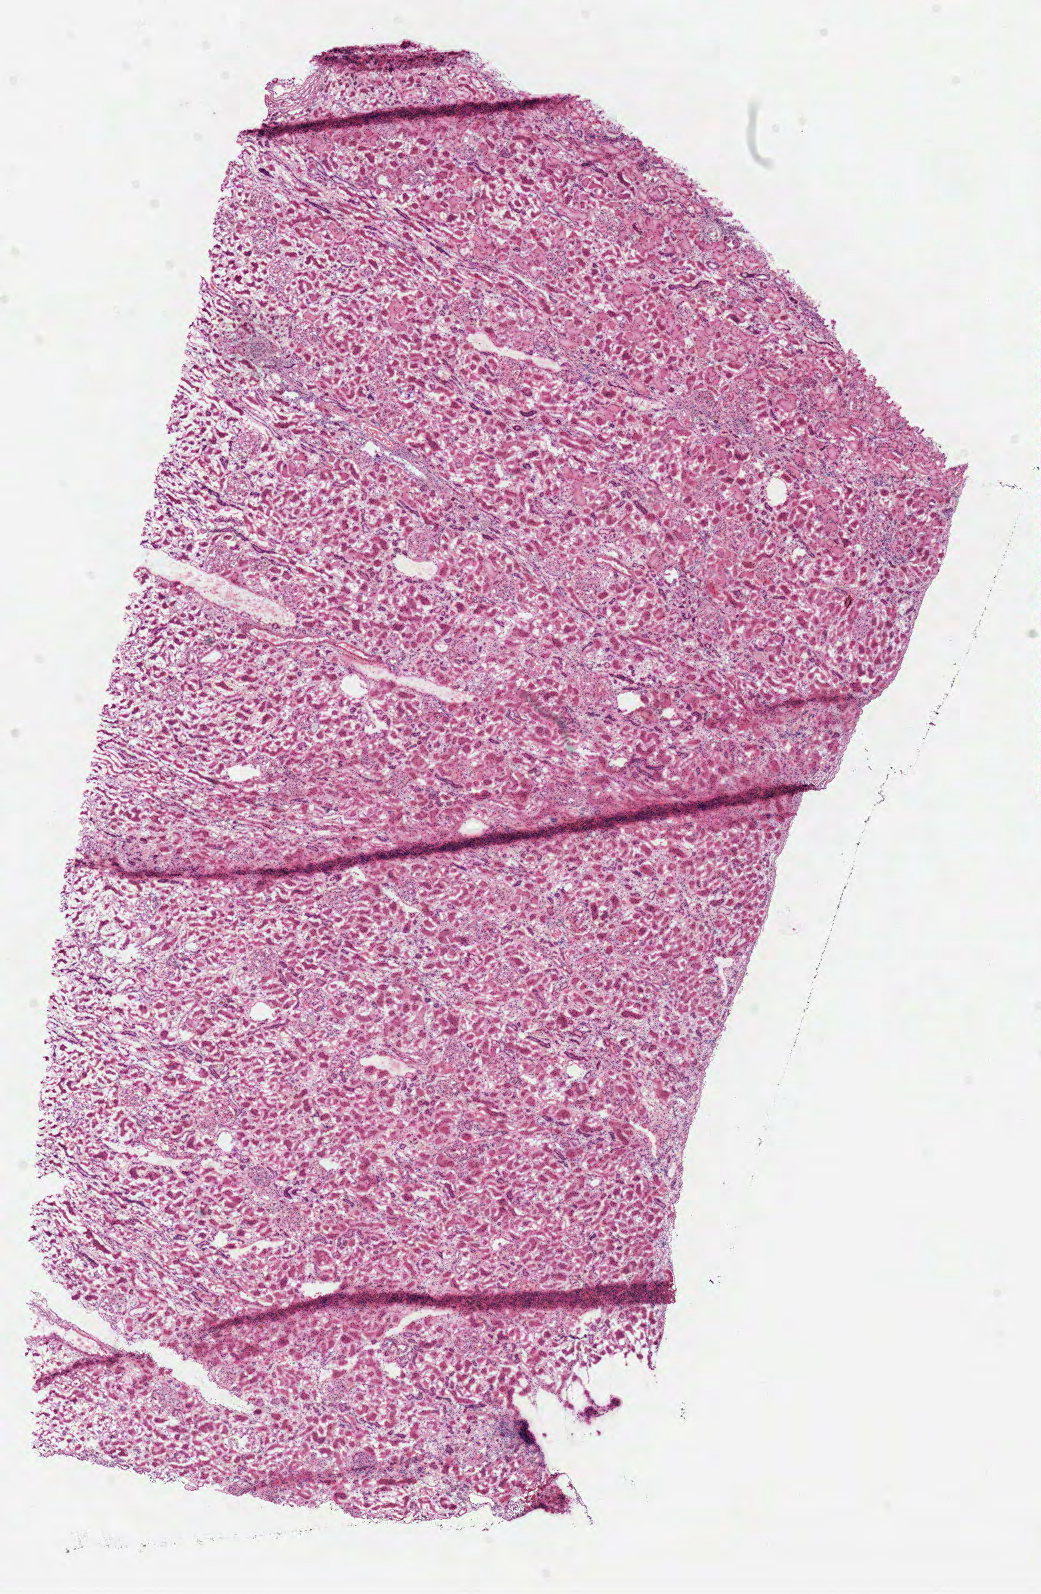
Whole-slide histology image, Hematoxylin and eosin (H&E) stained, shown as a low-resolution overview of the whole scanned area (about 8.2 x 12.6 mm). Frozen section from the top of the tissue portion. Solid tissue normal (non-tumour tissue) sample from the kidney. Male patient; age at initial diagnosis 68 years.
This section: solid tissue normal (non-tumour) sample from the same patient. Patient diagnosis: Clear cell adenocarcinoma, NOS.